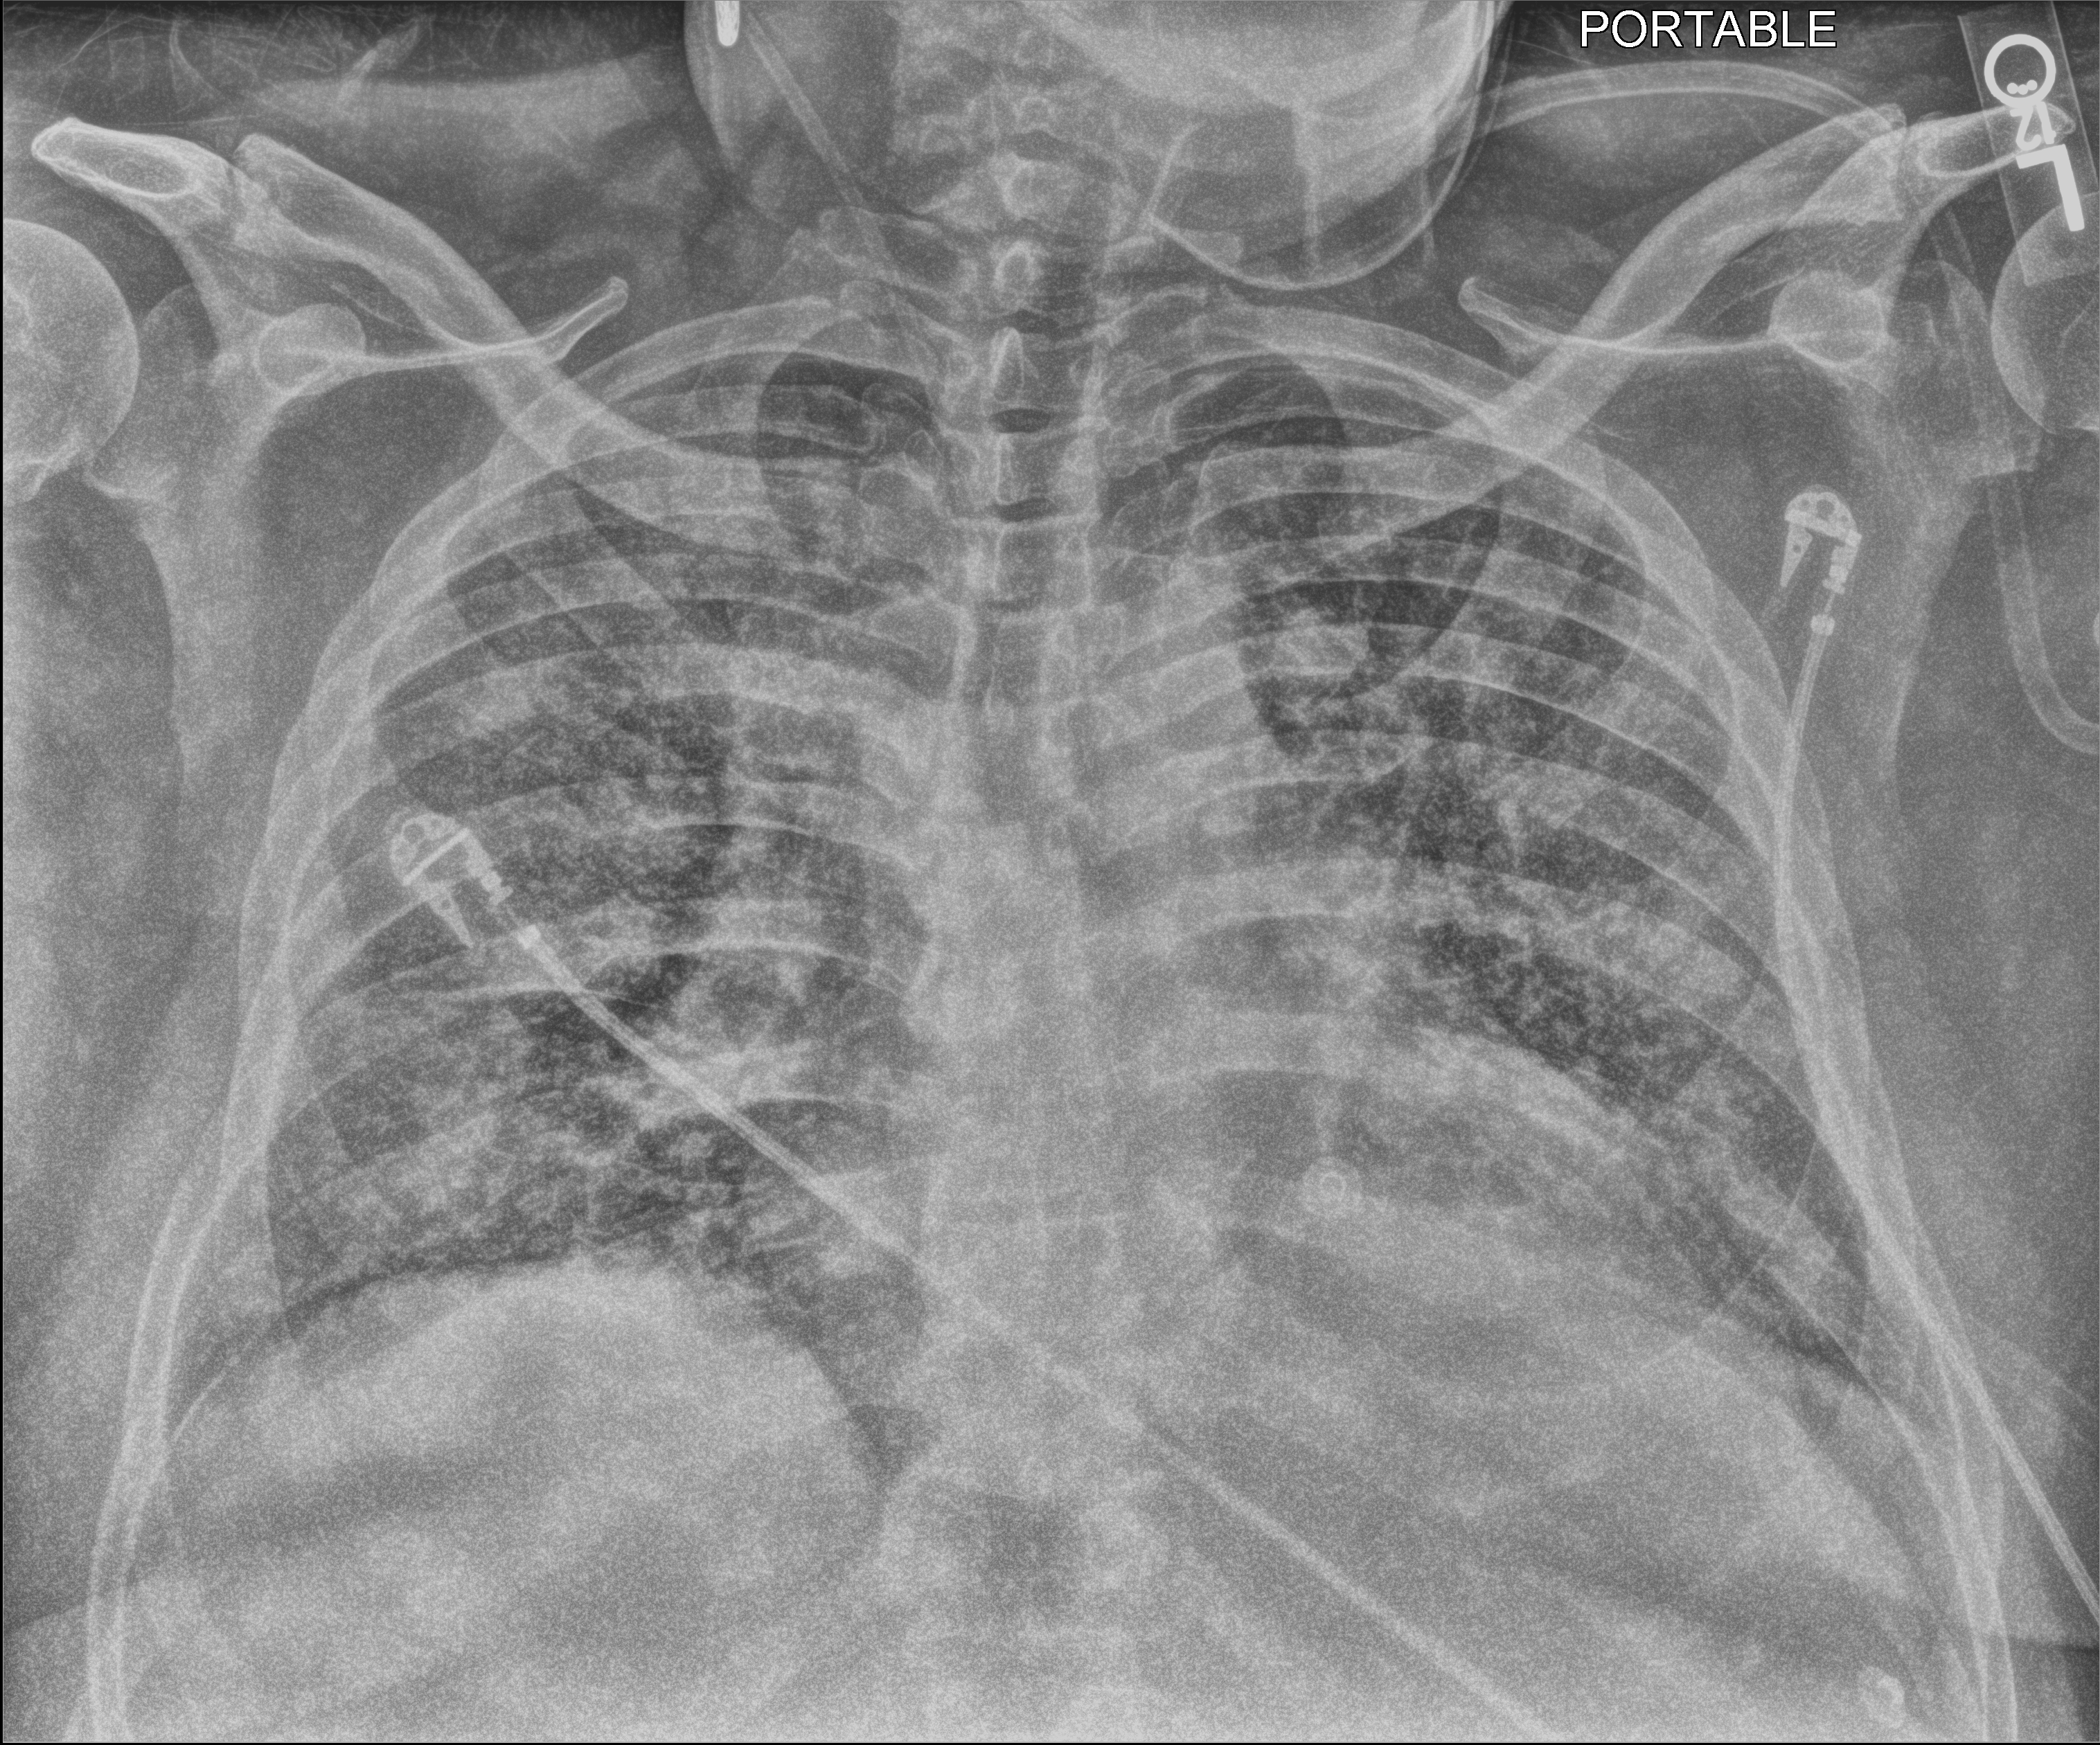
Chest X-ray (portable), anteroposterior (AP) projection. Male patient hospitalised with COVID-19, age 60–74 years.
Hospital-stay facts (about this admission, not read from this image; timing relative to this image not recorded): admitted to intensive care during this hospital stay: yes; chronic kidney disease (admission record): no.